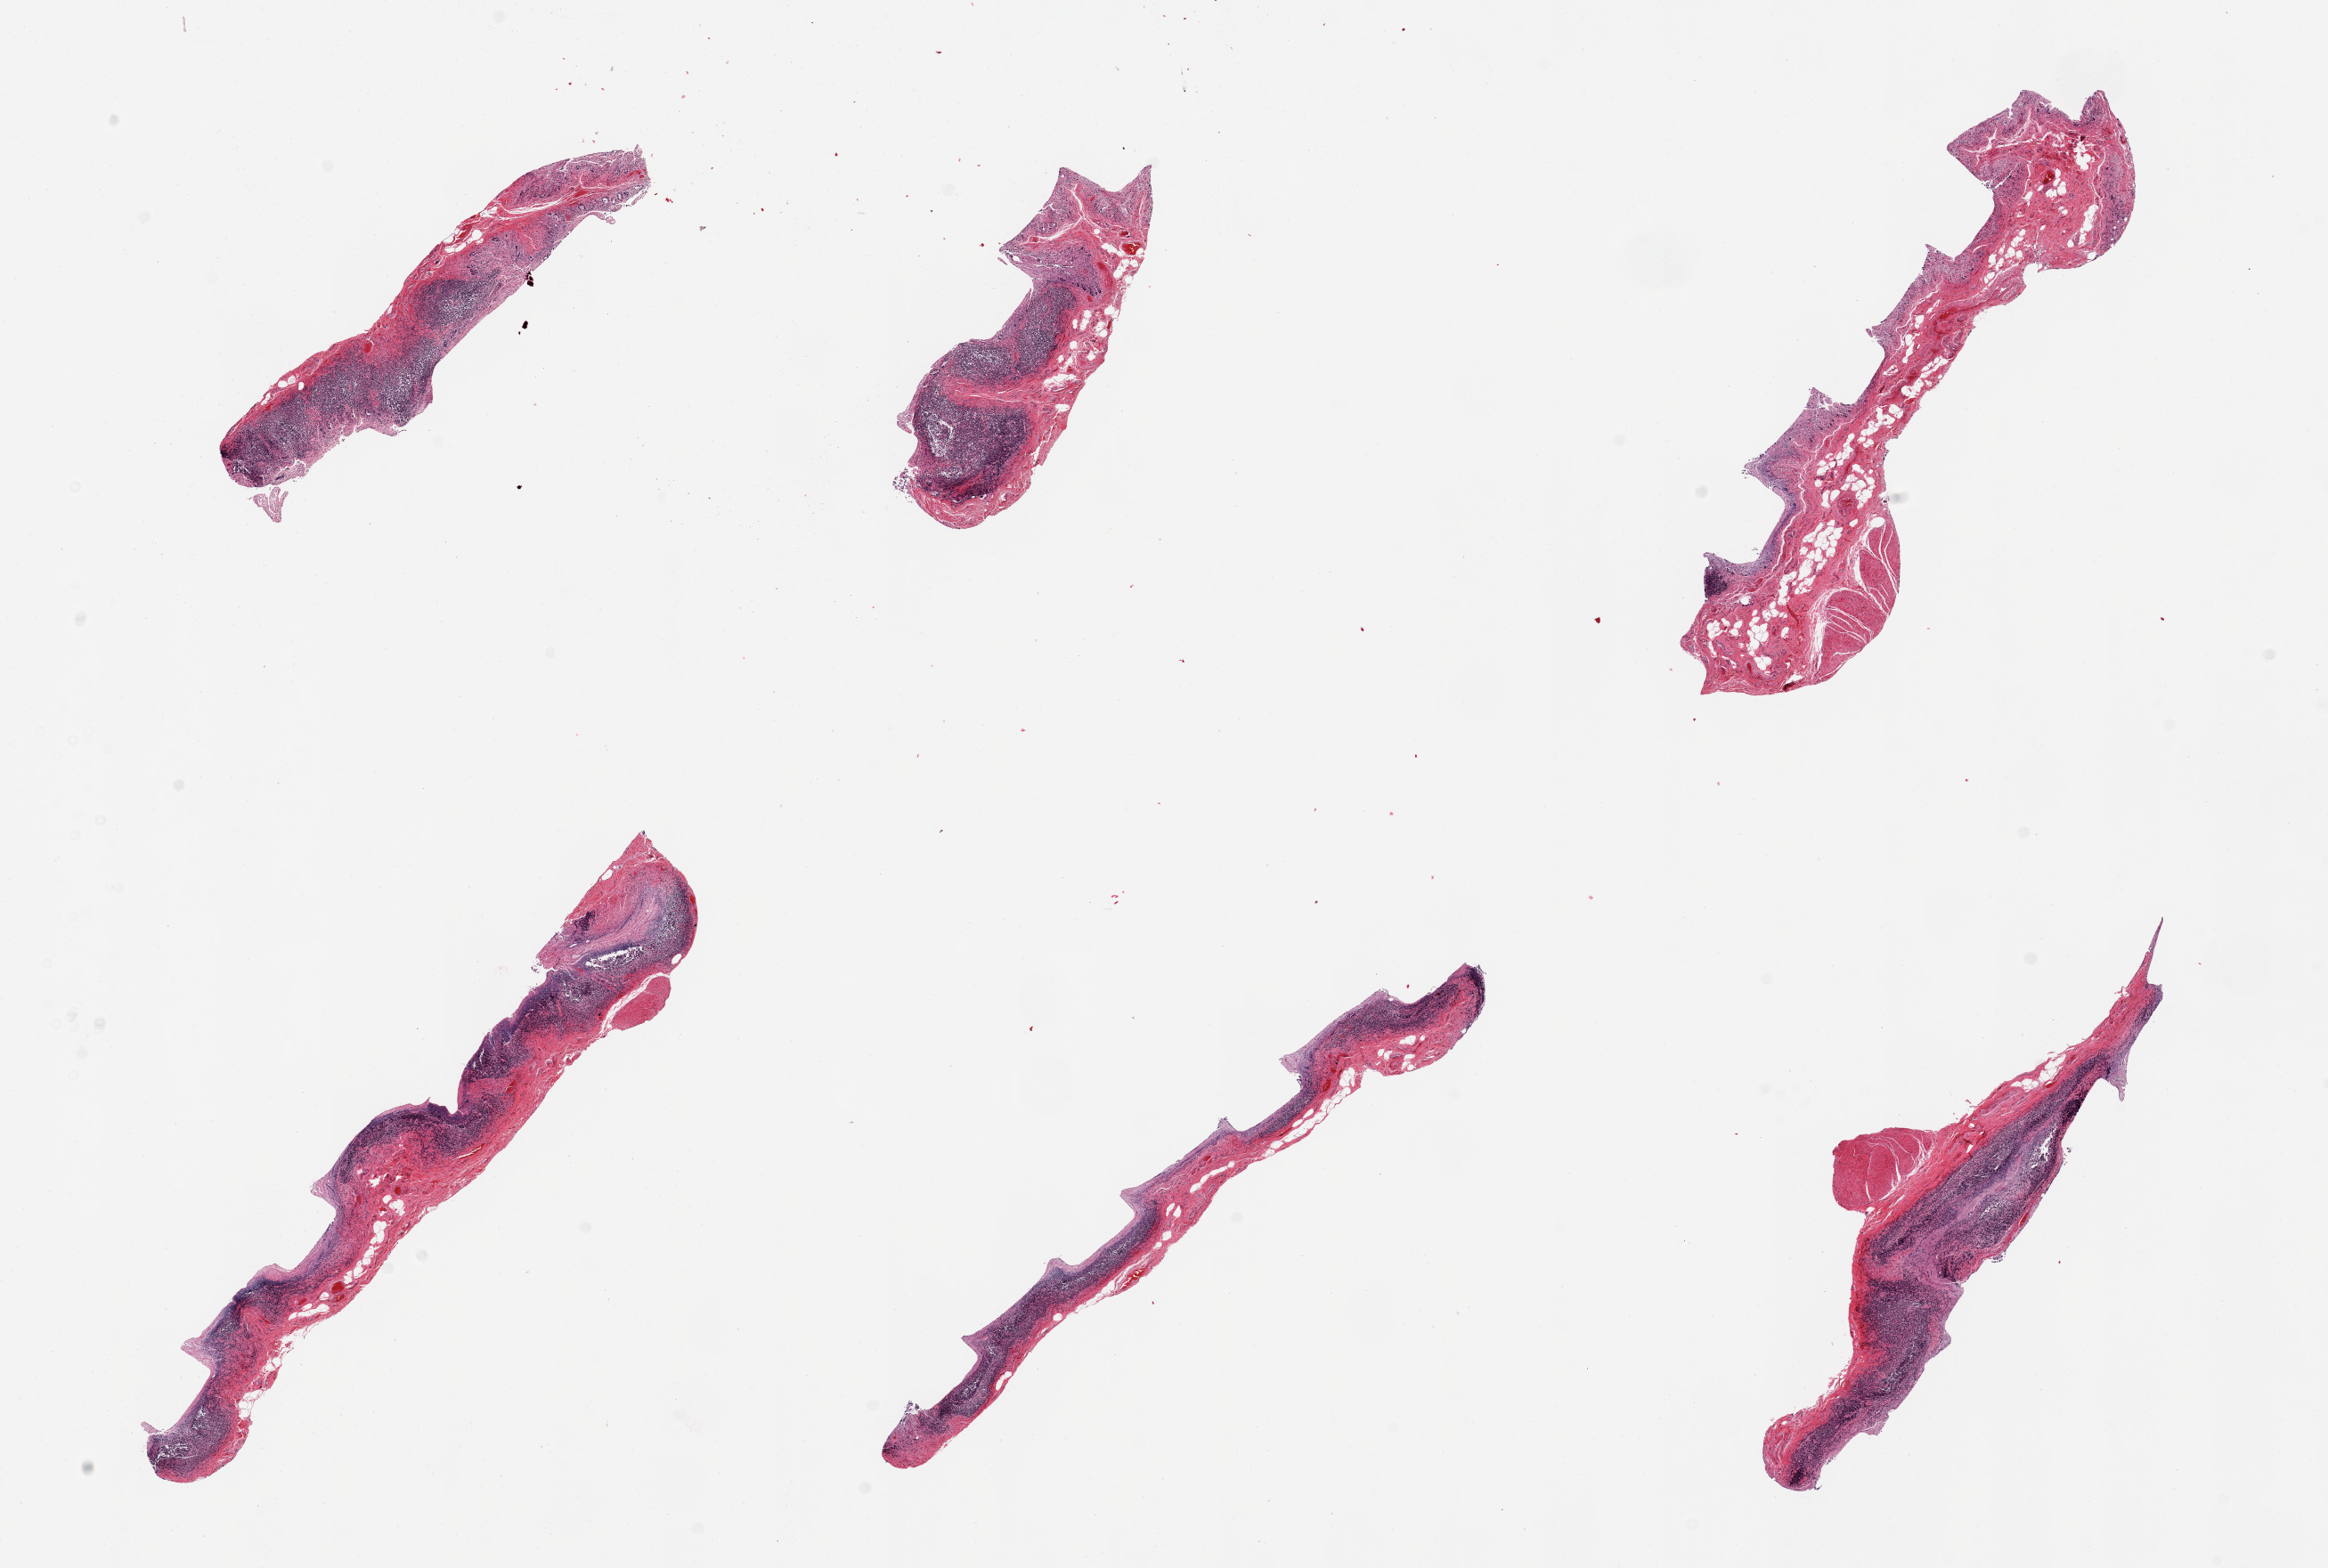
Digitized hematoxylin and eosin (H&E)-stained section, low-resolution overview of the scanned area, about 20.7 x 13.9 mm (slide scanned at 20x), PAXgene-fixed paraffin-embedded (PFPE) section, target tissue: ileum, tissue donor sample. Donor sex: male.
Pathologist's review note for this sample: 6 pieces; lymphoid tissue in all.